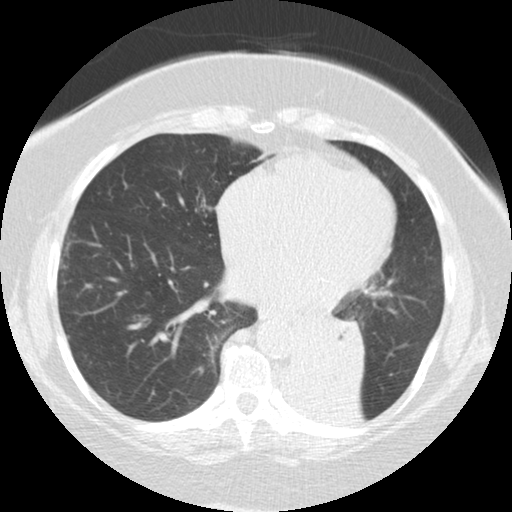
Low-dose screening chest CT, axial slice. Baseline screening round. Lung window (W 1500 / L -600 HU). Slice 79 of 136 in the series. 512 × 512 image matrix, field of view 309 × 309 mm. Female participant, aged 71 years at enrolment.
- Expert-annotated lung lesion, bounding box [x1, y1, x2, y2] px = [280, 302, 370, 384].
- Reader record for this screening exam (exam-level; its link to the box is not recorded): non-calcified nodule or mass ≥4 mm, right middle lobe, 5 × 5 mm, smooth margins, soft tissue attenuation.
- Note: the box lies in the patient's left hemithorax on this image, whereas the reader's record names the right lung; they may be different findings.
- Official screen result: positive, change unspecified: nodule(s) >= 4 mm or enlarging nodule(s), mass(es), or other non-specific abnormalities suspicious for lung cancer.
- Lung cancer was diagnosed 46 days after this screen: large cell carcinoma, NOS, left lower lobe, mediastinum, other location, poorly differentiated (G3), stage IV (AJCC 6th edition), 50 mm at pathology.